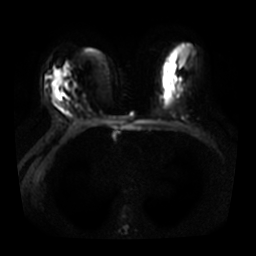
Breast MRI, one axial slice; slice 17 of 31 in the series (ordered by position); diffusion-weighted series; image 2 of 4 stored at this slice position (different b-values; order by instance number); 3 T; 5 mm slice thickness; 256 × 256 image matrix, field of view 350 × 350 mm. Female patient.
Annotated regions visible in this slice (outlined manually by an expert reader):
- tumour on diffusion-weighted imaging: bounding box (x1, y1, x2, y2) in pixels: (53, 71, 61, 89)